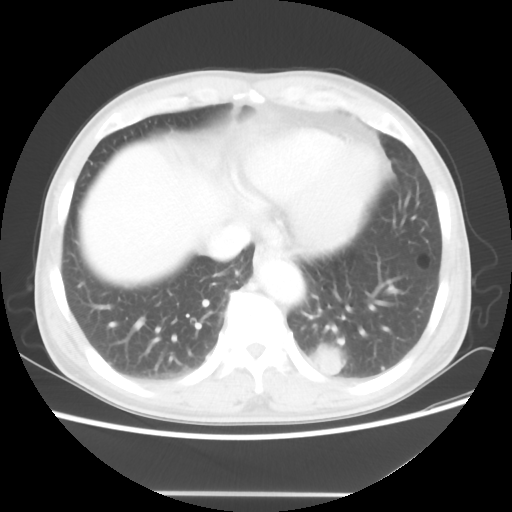
Chest CT, one axial slice. Reconstruction kernel STANDARD. 100 kVp. Lung window (W 1500 / L -600 HU). 5 mm slice thickness. 512 × 512 image matrix, field of view 360 × 360 mm. Patient: male, 55 years. Case-level facts recorded for this patient, not image findings: clinical TNM (as recorded): T1c N3 M0; histopathological grade: G3.
Structures marked on this image (rectangle marked by the reading radiologist):
- lung tumour (recorded histology: small cell carcinoma): bounding box [x1, y1, x2, y2] px = [306, 339, 345, 380]